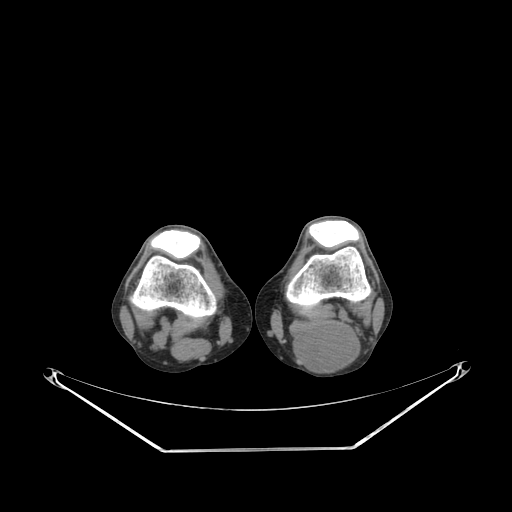
CT of an extremity soft-tissue mass (from a PET/CT study), one axial slice. Position 183 of 267 along the scan axis. Reconstruction kernel SOFT. Soft-tissue window (W 400 / L 40 HU). 512 × 512 image matrix. Male patient. From the clinical record (not read from this slice): histological type: synovial sarcoma; site of the primary tumour: left poplietal fossa.
Structures marked on this image (expert contour drawn on MRI and transferred to this co-registered scan by the dataset authors):
- gross tumour volume (mass): box from (x=290, y=324) to (x=362, y=373) px